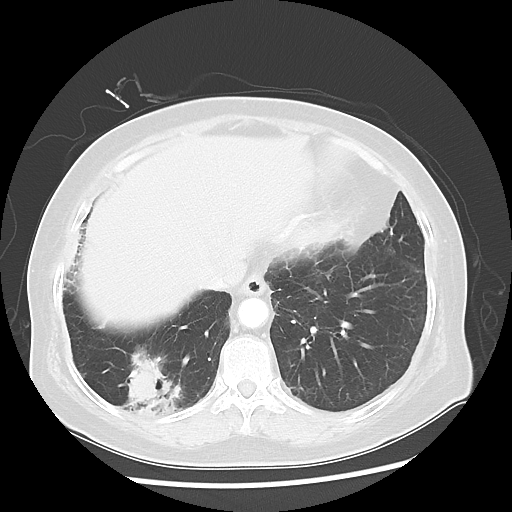
Chest CT, one axial slice. Slice 15 of 56 in the series (ordered by position). Reconstruction kernel LUNG. Lung window (W 1500 / L -600 HU). 5 mm slice thickness. 512 × 512 image matrix, field of view 360 × 360 mm. Female patient, age 64 years. Case-level facts recorded for this patient, not image findings: clinical TNM (as recorded): Tis N0 M0.
Structures marked on this image (bounding box drawn by a radiologist):
- lung tumour (recorded histology: adenocarcinoma): bounding box [x1, y1, x2, y2] px = [119, 339, 195, 438]